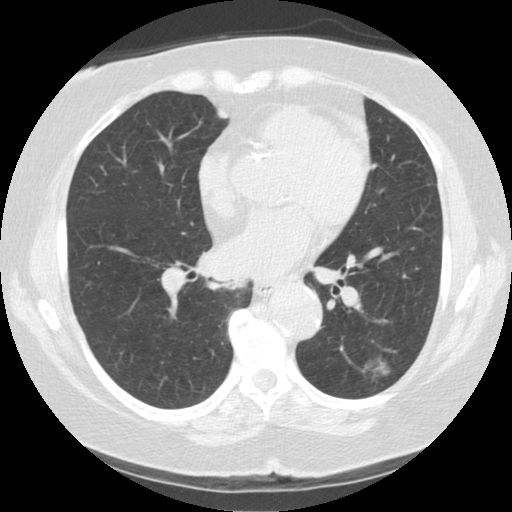
Low-dose screening chest CT, one axial slice; slice 64 of 122 in the series (ordered by position); reconstruction kernel STANDARD; 140 kVp; lung window (W 1500 / L -600 HU); 512 × 512 image matrix, field of view 329 × 329 mm.
Annotated regions visible in this slice (manually delineated by an expert):
- lesion 1 (tumor, lower lobe of left lung): box from (x=365, y=354) to (x=390, y=377) px